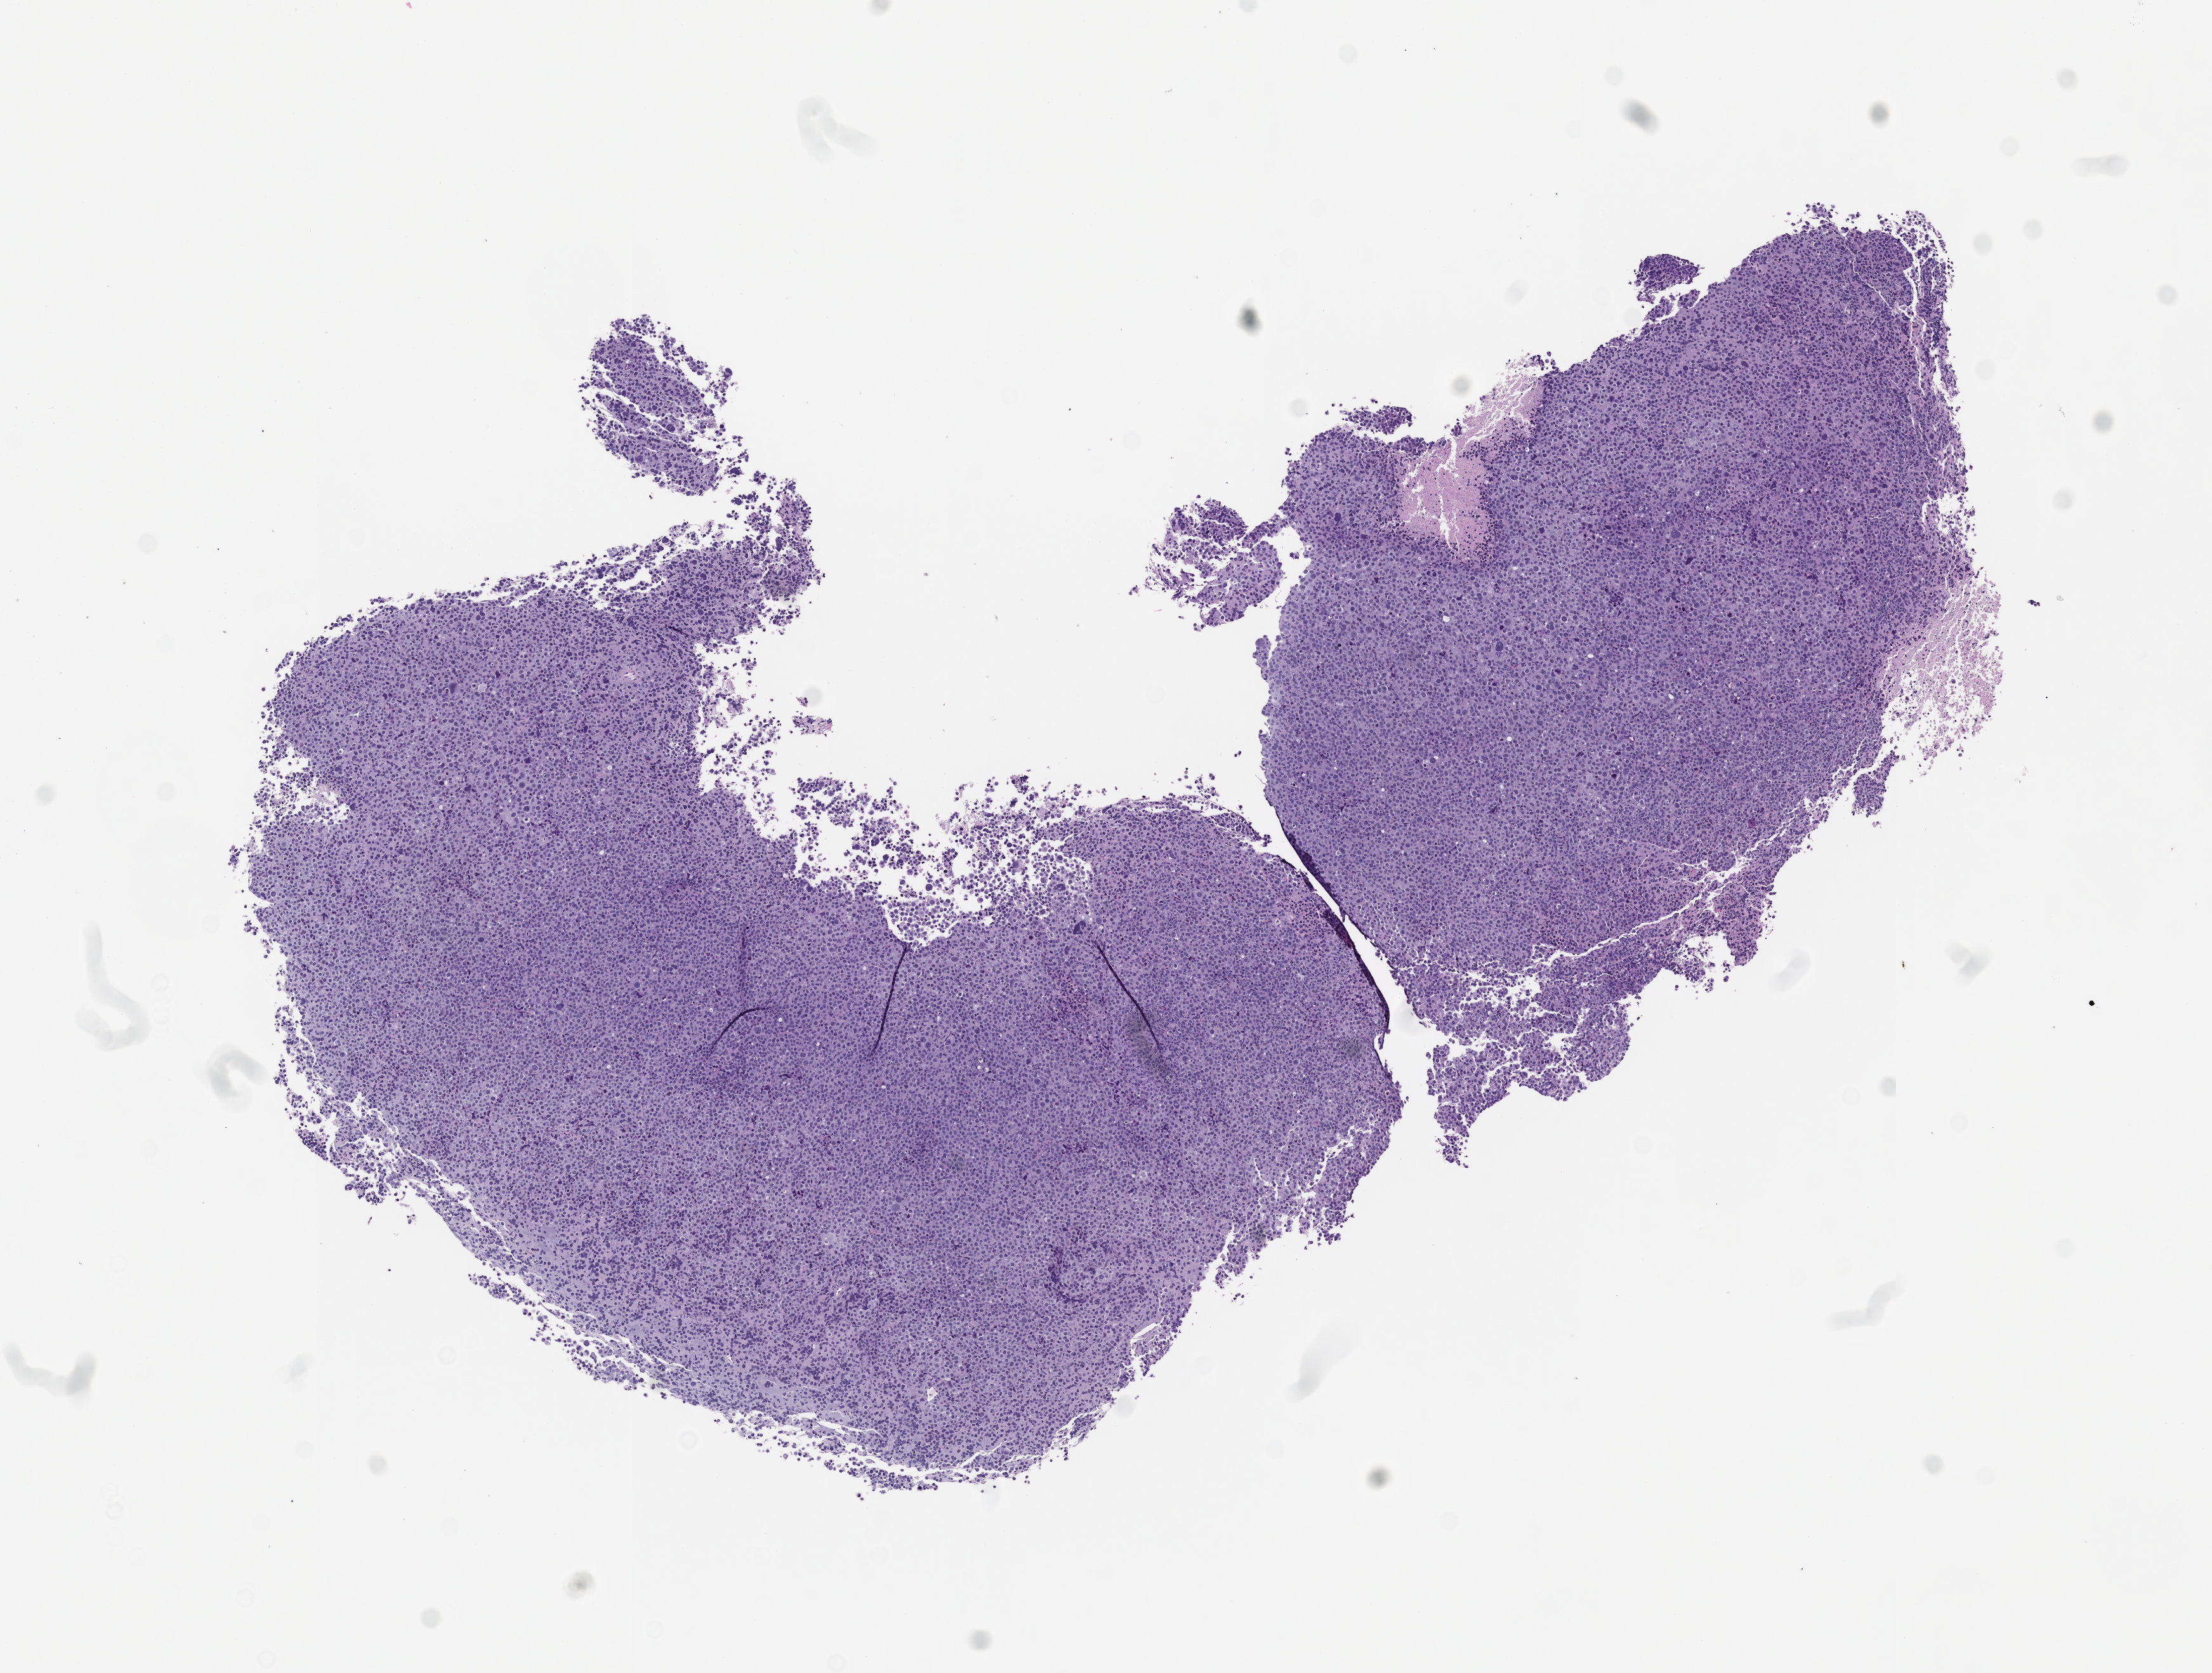
Hematoxylin and eosin (H&E) whole-slide image of a patient-derived xenograft (PDX) tumor grown in a mouse, passage 4 — shown as a low-resolution overview of the whole scanned area (about 7.0 x 5.3 mm), formalin-fixed paraffin-embedded section, originating tumor site category: bladder.
Originating patient diagnosis: Urothelial Carcinoma.